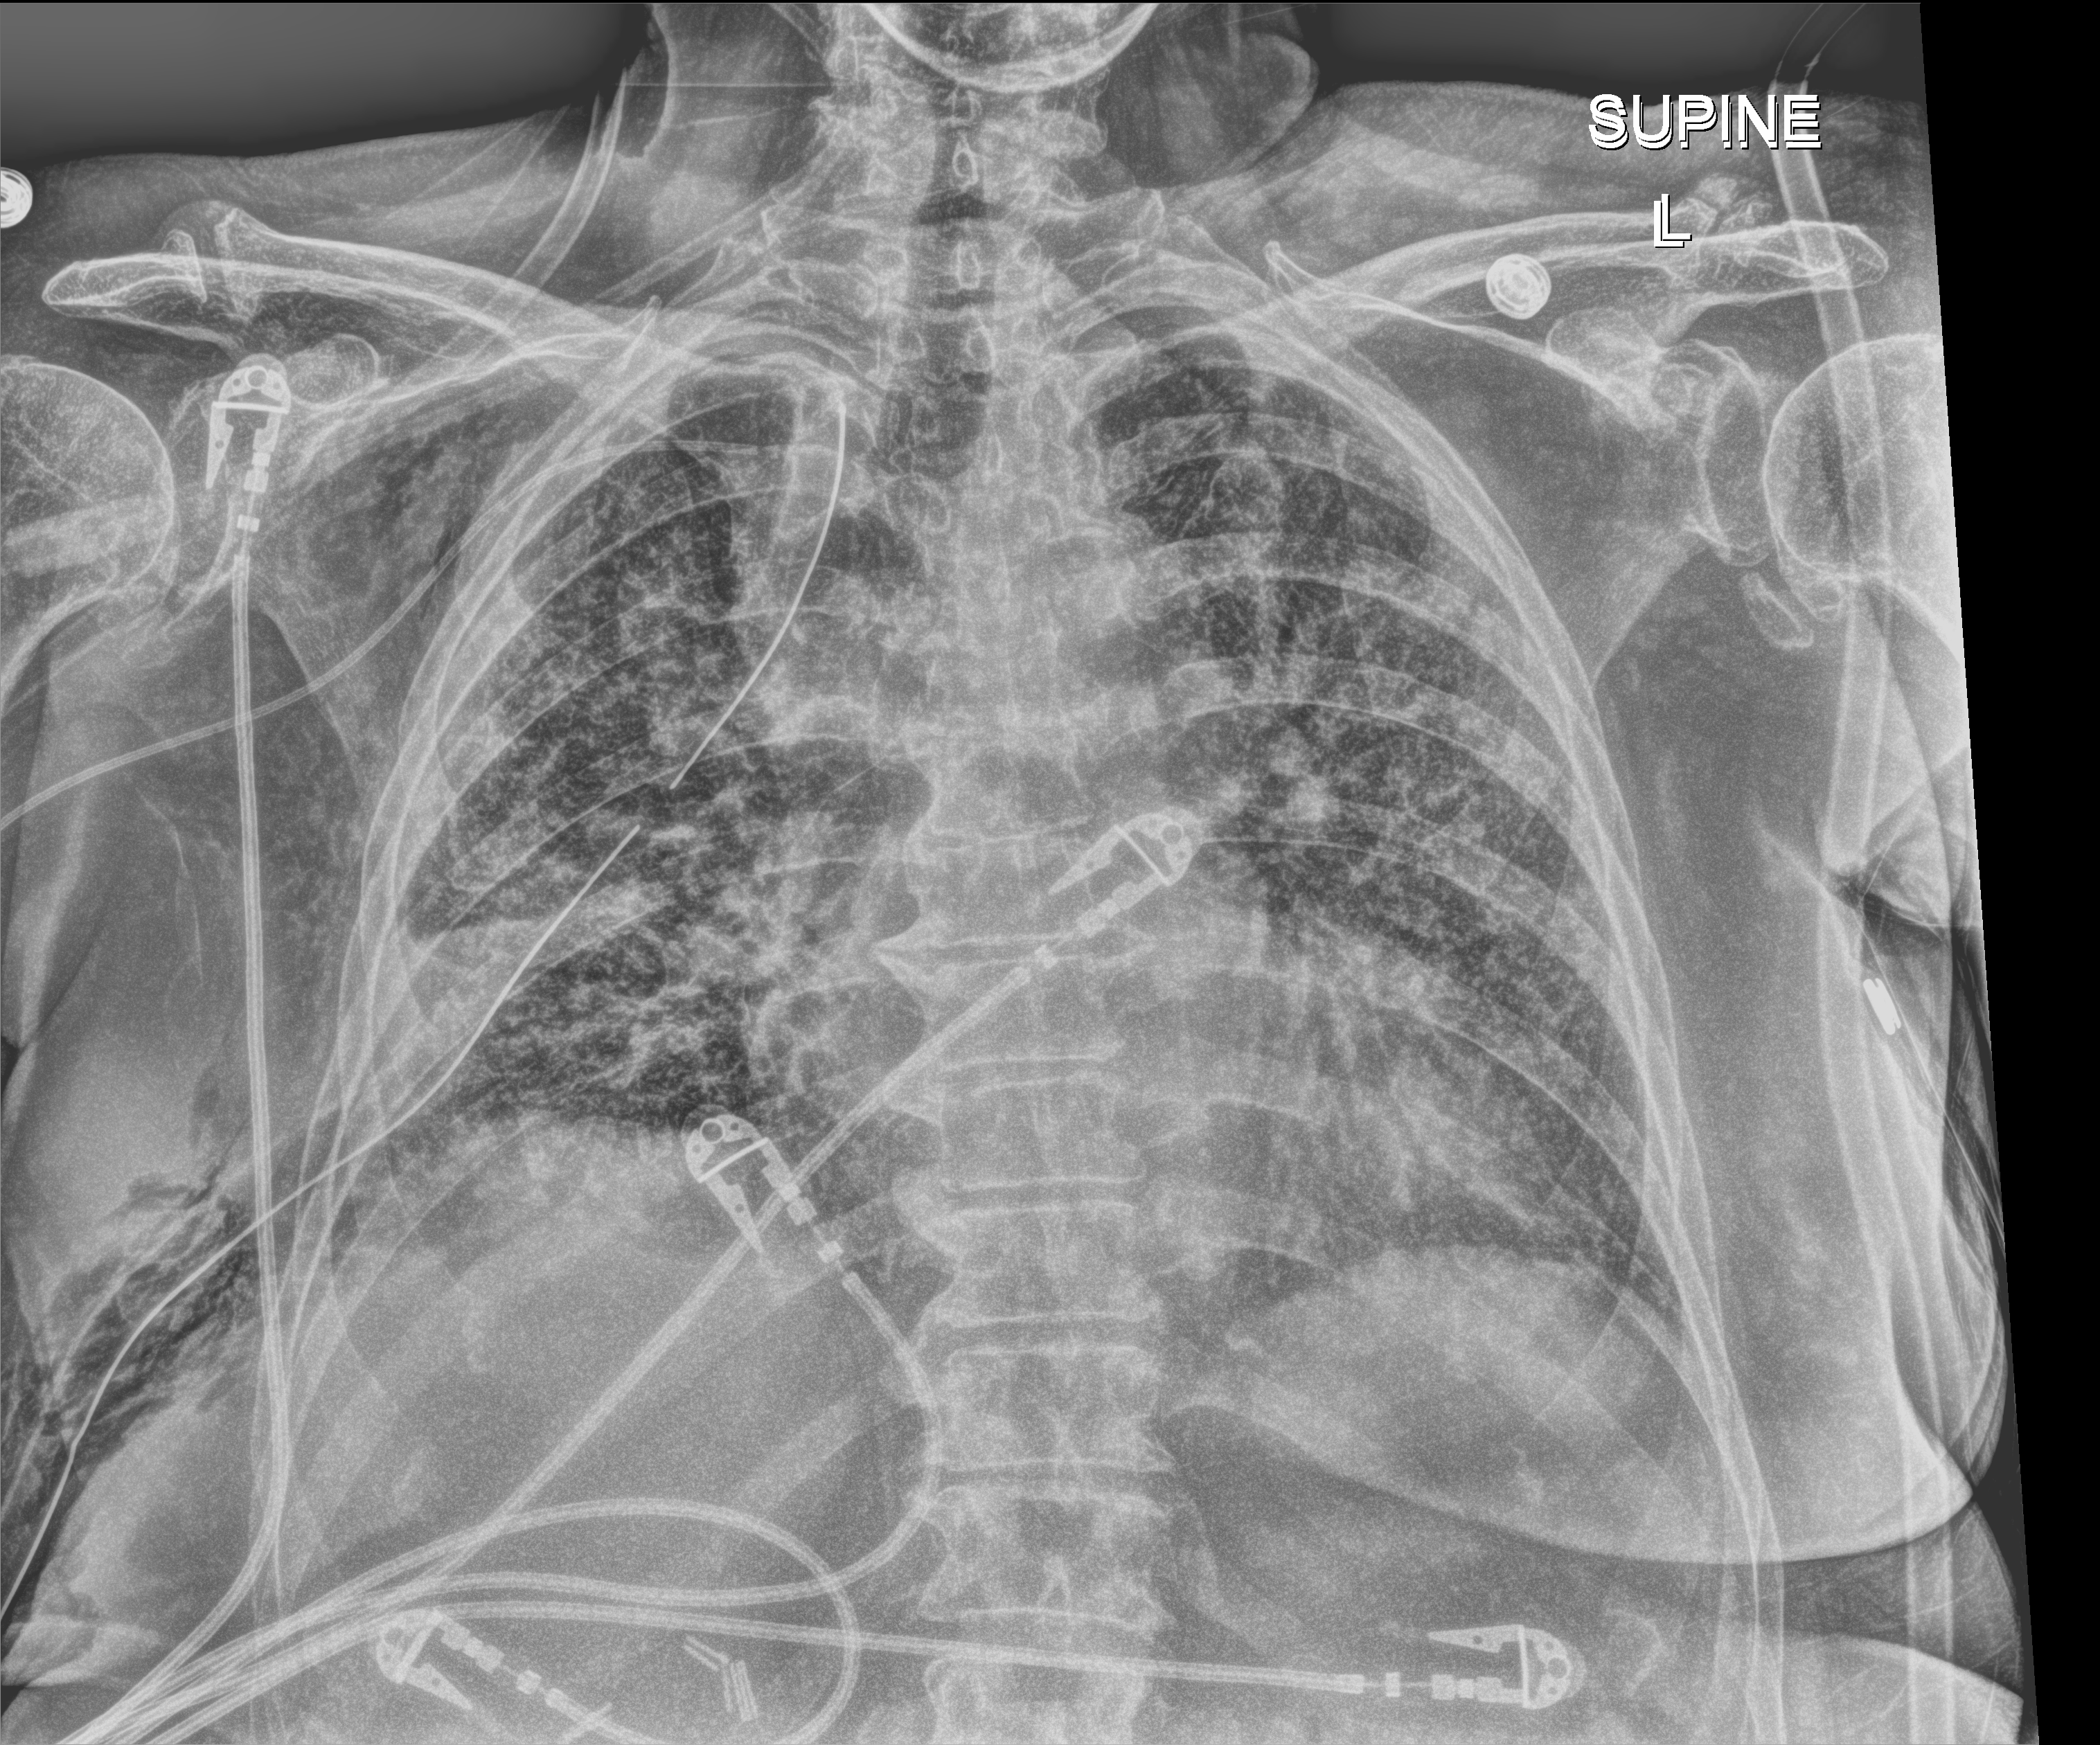
Chest radiograph. Patient hospitalised with COVID-19; female, aged 75–90 years.
From the hospital-stay record, not from the radiograph (when in the stay this image was taken is not recorded):
- chronic kidney disease (admission record): no
- admitted to intensive care during this hospital stay: no
- mechanically ventilated during this hospital stay: yes